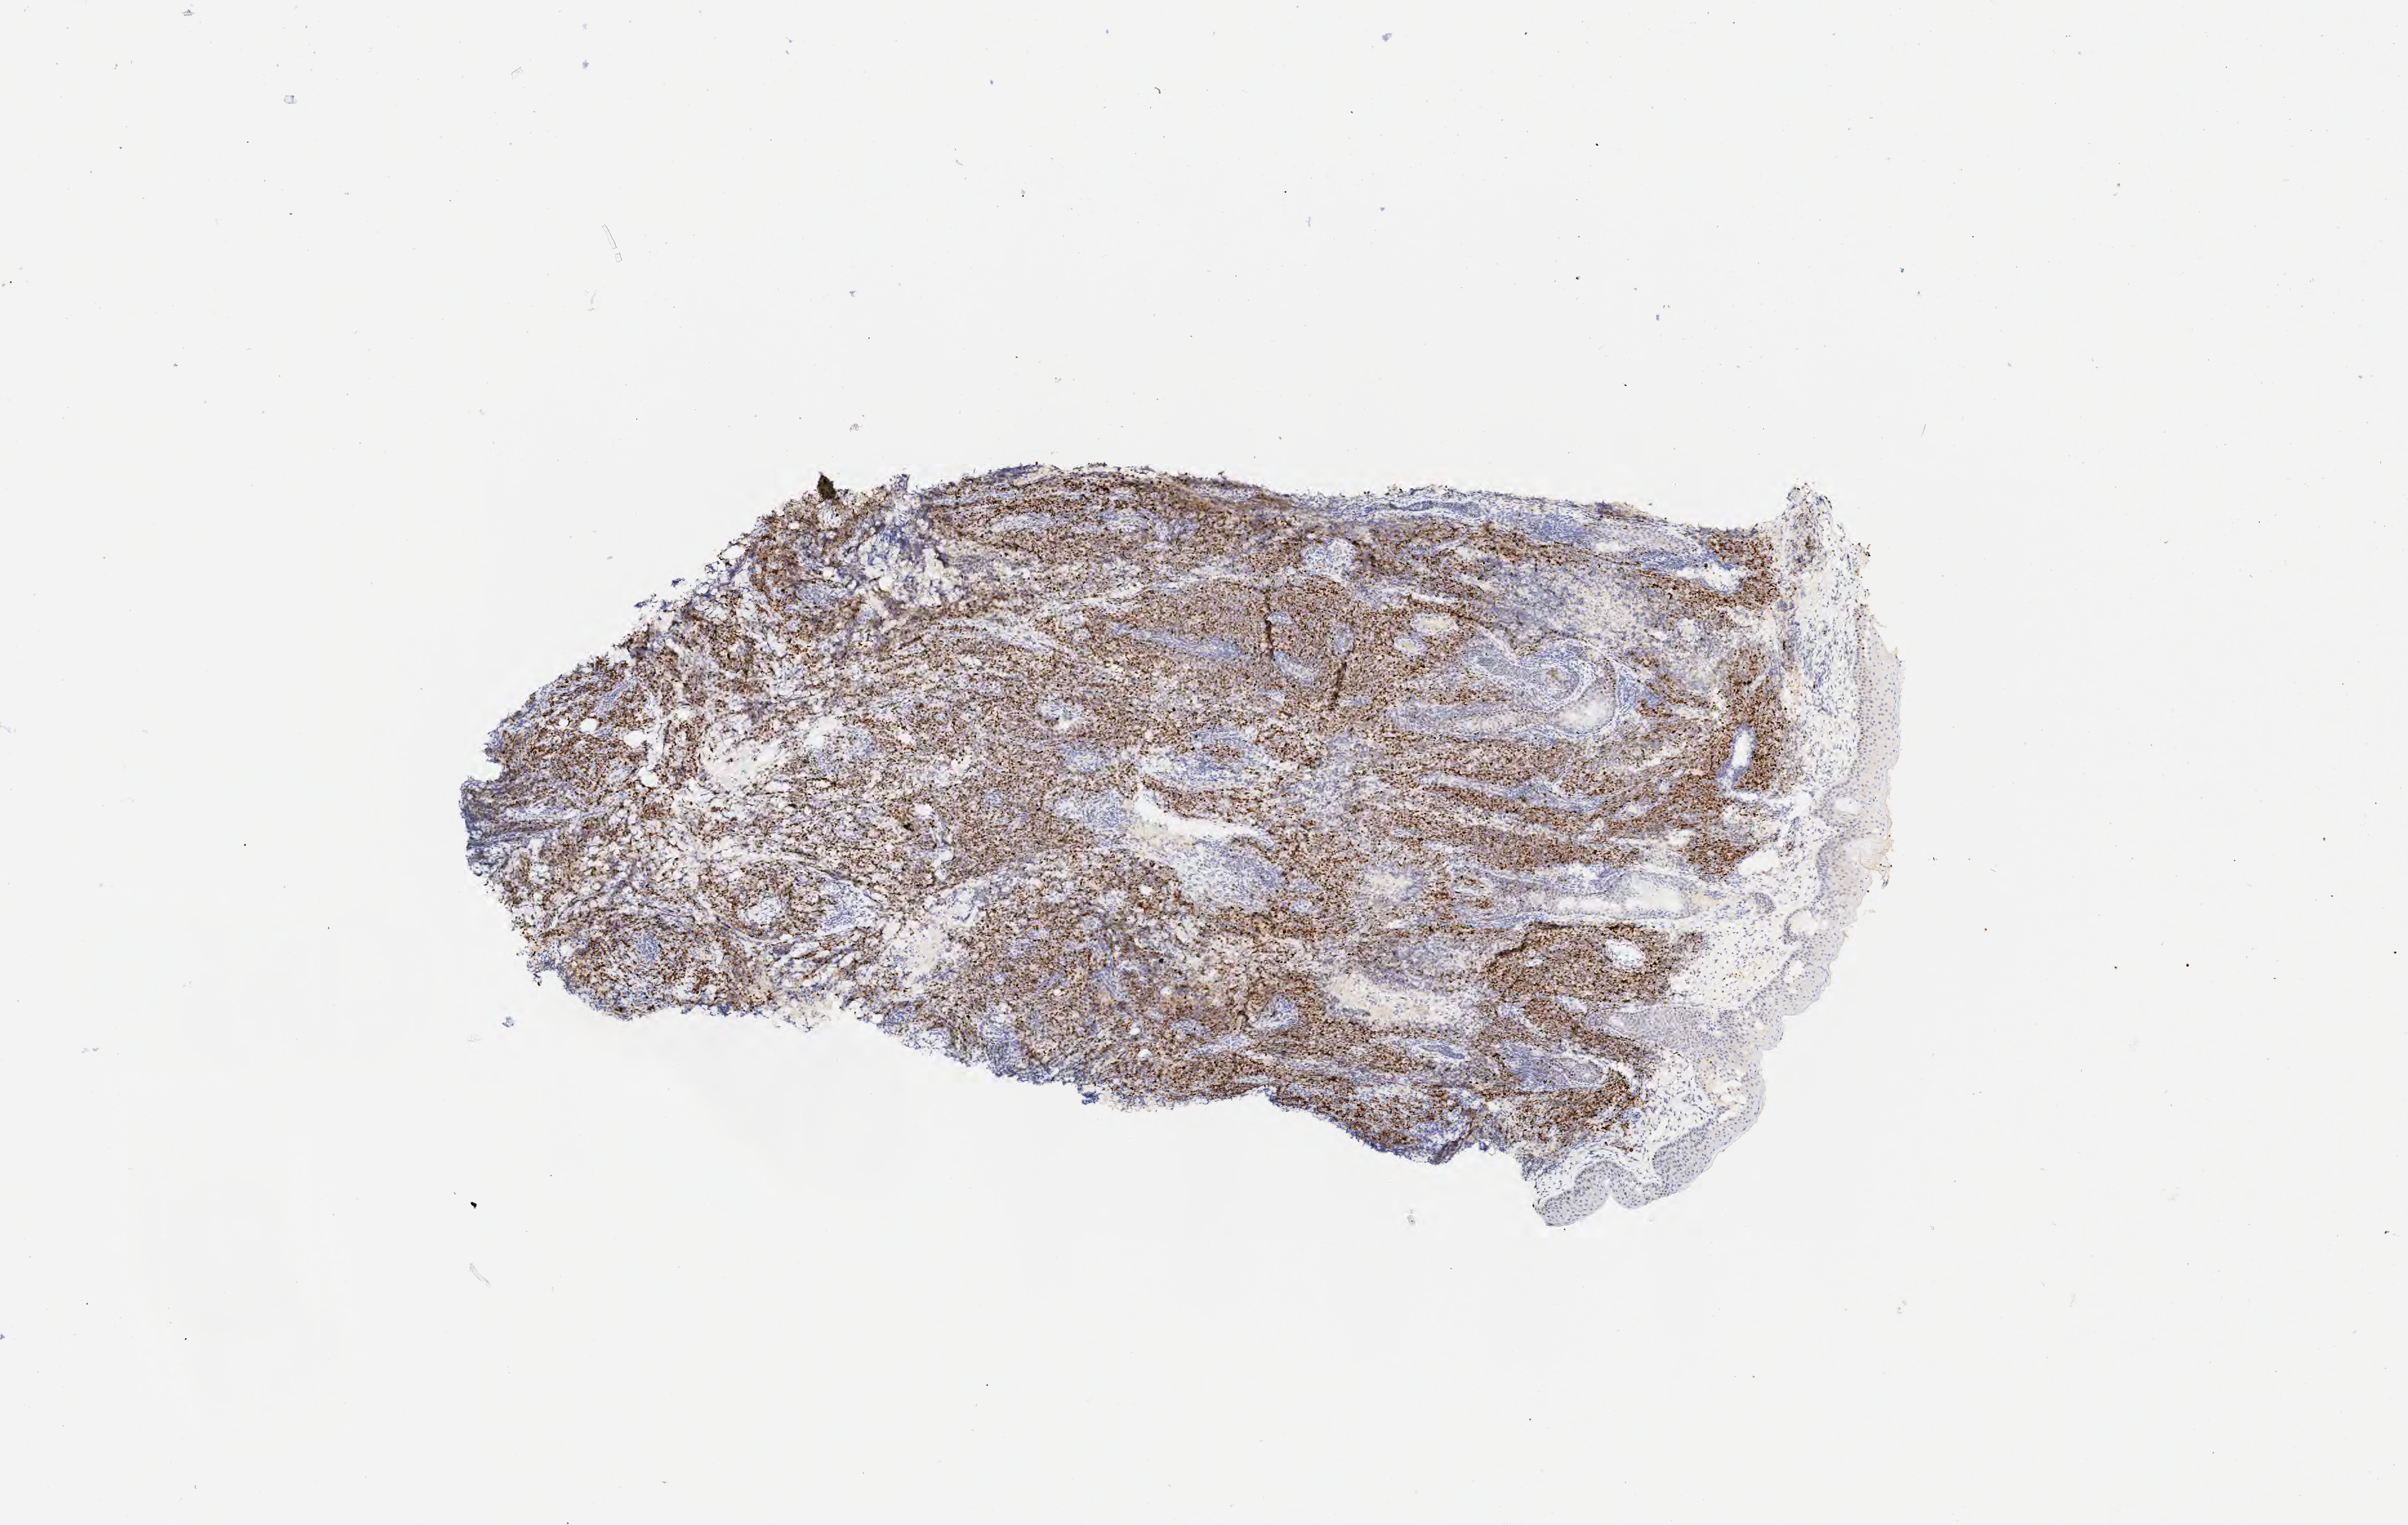
Whole-slide image, immunohistochemical stain for p53, whole scanned area (about 7.5 x 4.8 mm) shown as a low-resolution overview, specimen: tumor tissue. Male patient, aged 41.
* histologic diagnosis: Diffuse large B-cell lymphoma, NOS